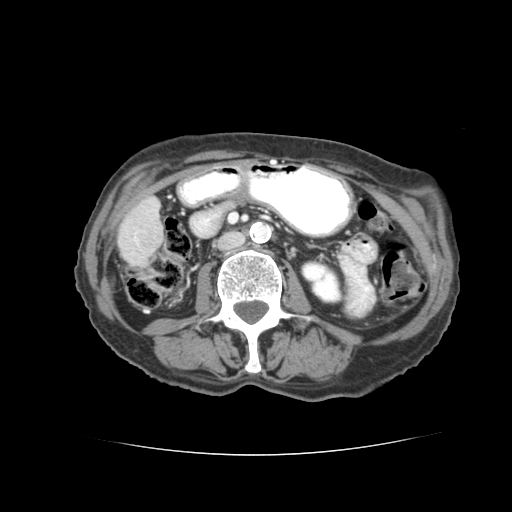
Contrast-enhanced abdominal CT (liver protocol), one axial slice. Position 11 of 77 along the scan axis. 120 kVp. Soft-tissue window (W 400 / L 40 HU). 2.5 mm slice thickness. 512 × 512 image matrix, field of view 340 × 340 mm. From the clinical record (not read from this slice): diagnosis: hepatocellular carcinoma (patient treated with transarterial chemoembolisation; whether this scan precedes or follows treatment is not stated here); TNM stage (as recorded): Stage-I; Child-Pugh class: A; tumour differentiation: well differentiated; tumour size: 7.6 cm.
Outlined on this slice (semi-automatically segmented with operator editing):
- liver parenchyma outside the tumour (the mass and vessels are separate outlines, so this box may not span the whole liver): bounding box [x1, y1, x2, y2] px = [117, 188, 158, 262]